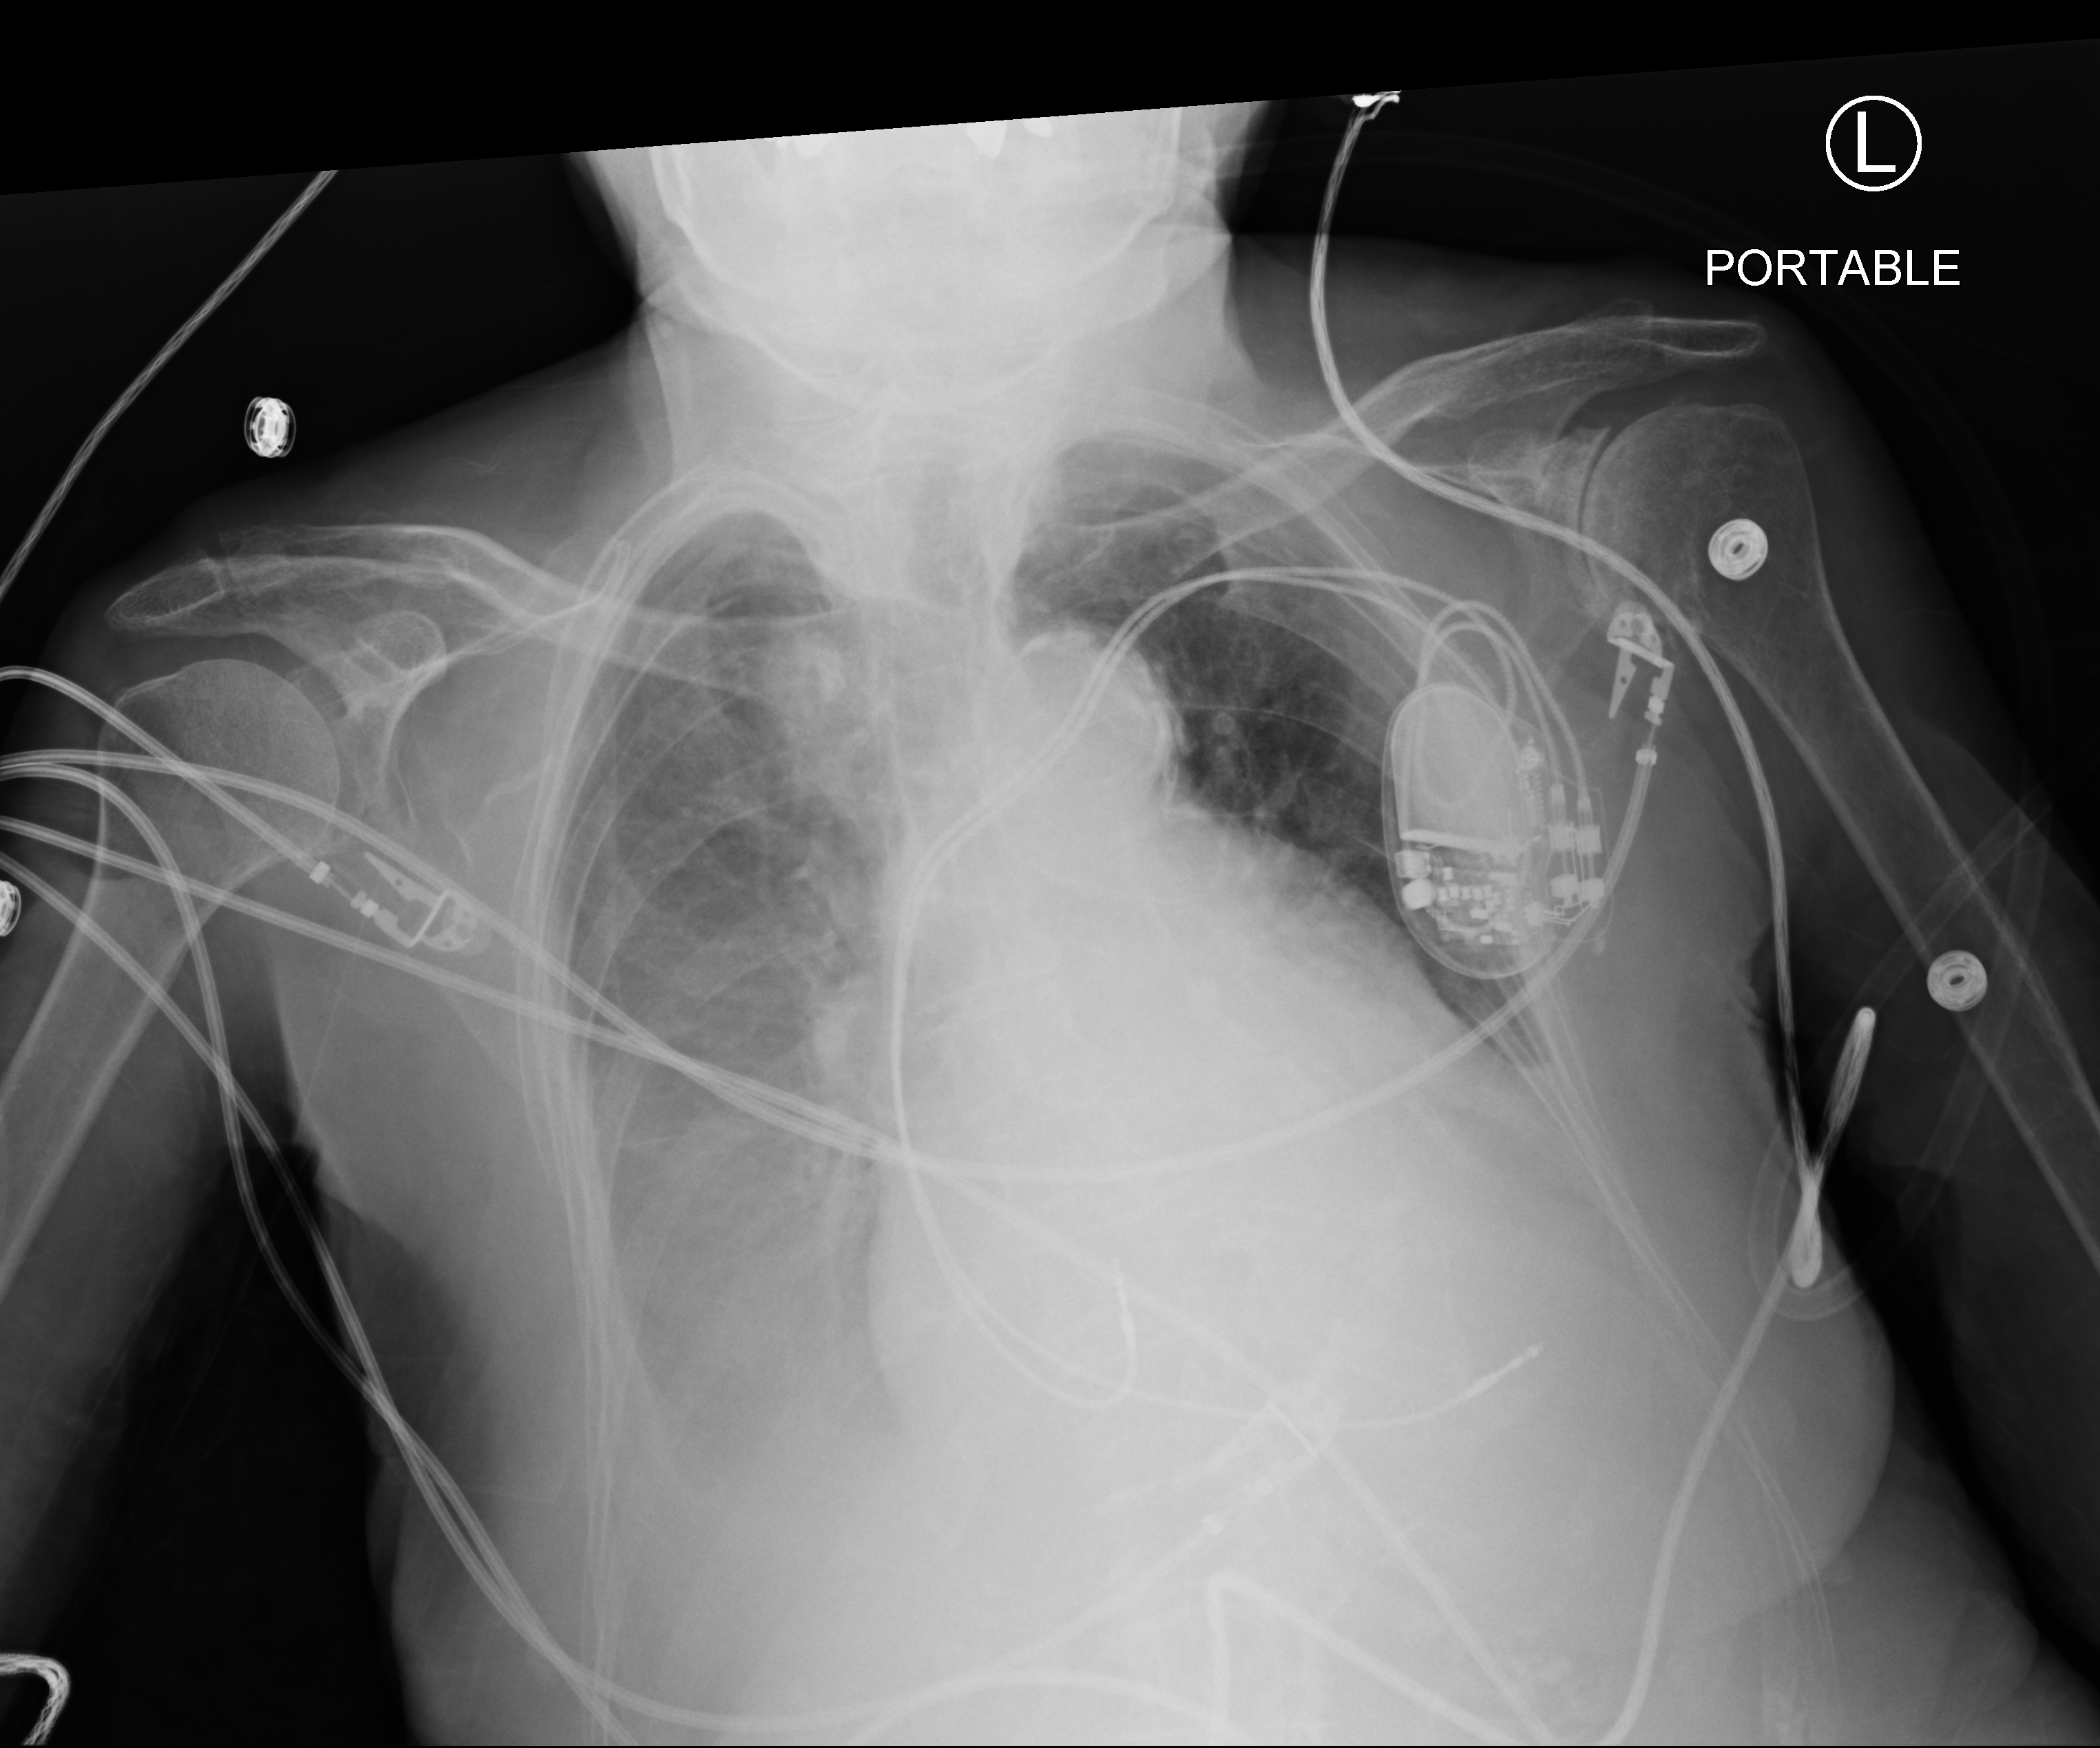
Portable chest radiograph; anteroposterior (AP) projection. Patient hospitalised with COVID-19; female, aged 75–90 years.
Admission-level facts for this patient (not findings on this image; timing relative to this image not recorded): admitted to intensive care during this hospital stay: no; length of hospital stay: 5 days.